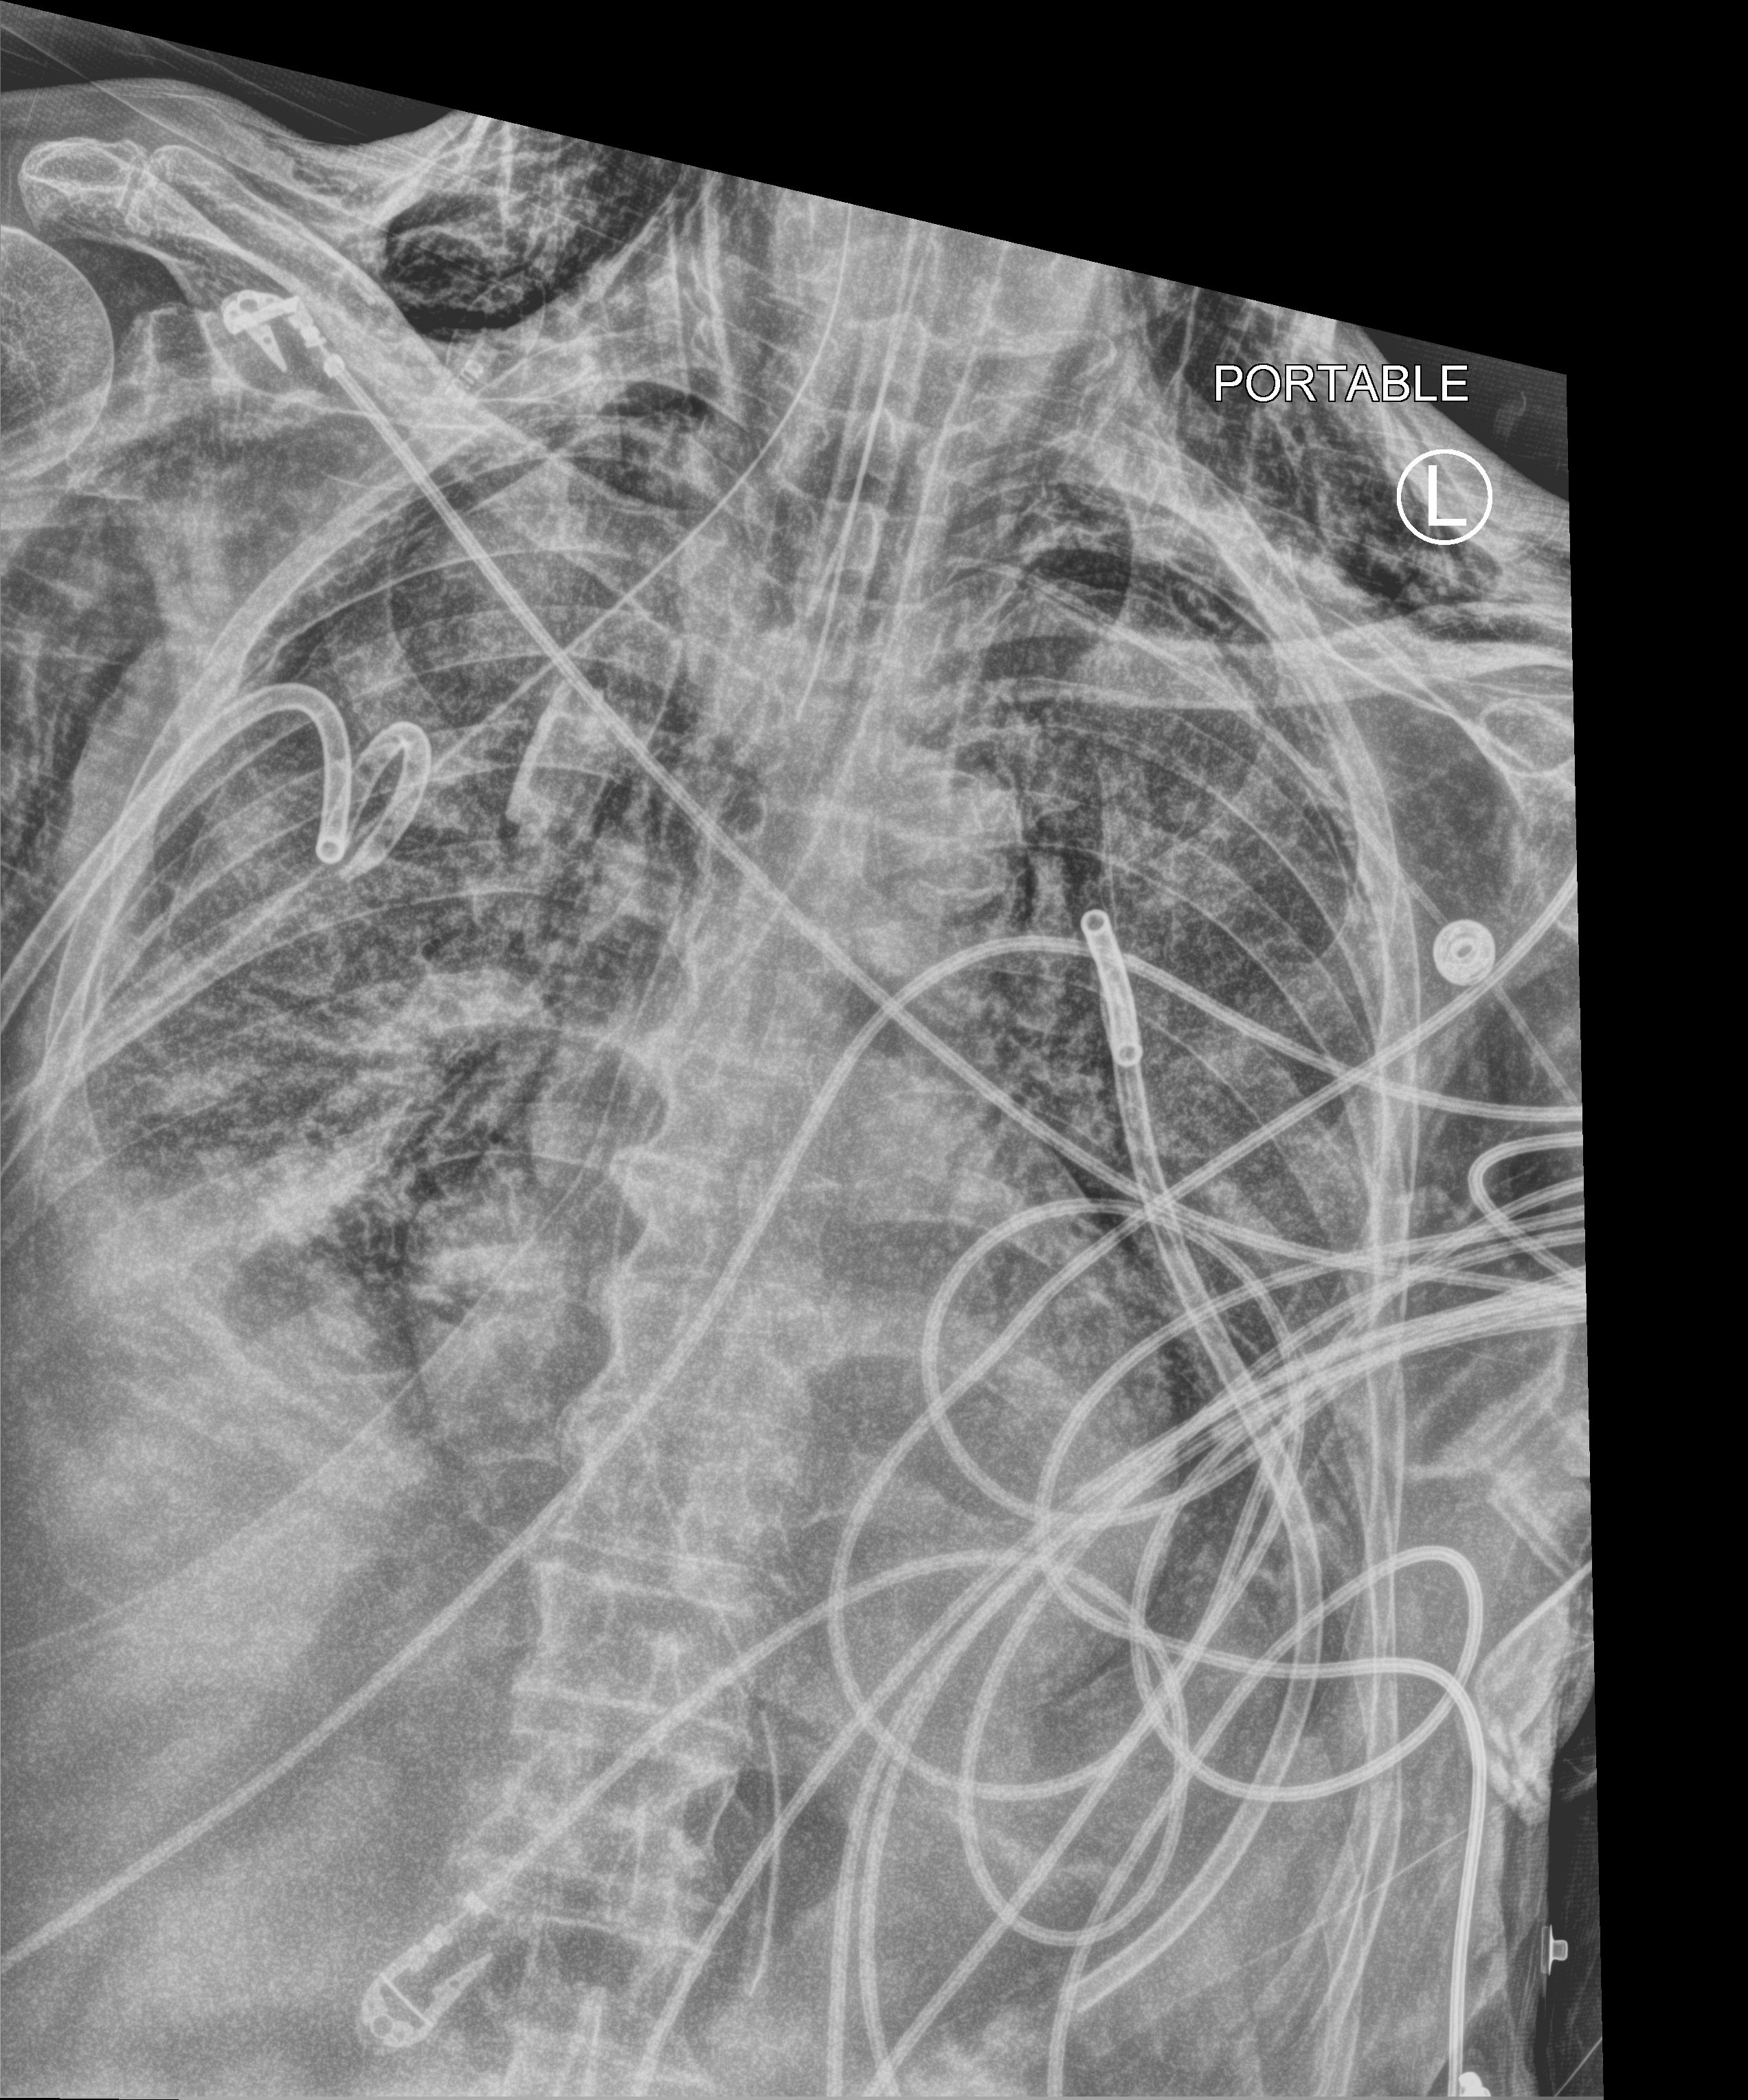
Chest X-ray (portable); anteroposterior (AP) projection. Male patient hospitalised with COVID-19, age 75–90 years.
From the hospital-stay record, not from the radiograph (when in the stay this image was taken is not recorded): hypertension (admission record): yes; length of hospital stay: 30 days.